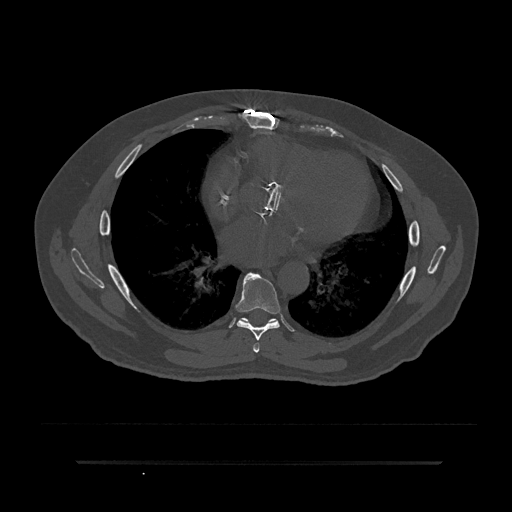
CT including the spine, one axial slice. Slice 469 of 797 in the series (ordered by position). Reconstruction kernel Br40s/3. 120 kVp. Bone window (W 1800 / L 400 HU). 0.5 mm slice thickness. 512 × 512 image matrix. Male patient, age 59 years. From the clinical record (not read from this slice): primary cancer: bile ducts; vertebrae with lytic lesions (as recorded): T10.
Outlined on this slice (semi-automatic segmentation, software-assisted and operator-edited):
- T6 vertebra: bounding box <253,343,260,353> (left, top, right, bottom; pixels)
- T7 vertebra: <235,272,280,341>
- T8 vertebra: <240,318,249,323>